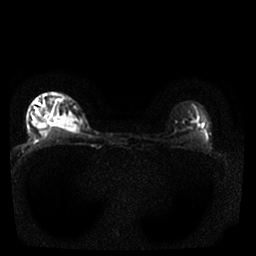
Breast MRI, one axial slice; slice 24 of 25 in the series (ordered by position); diffusion-weighted series; image 2 of 4 stored at this slice position (different b-values; order by instance number); 1.5 T; 4 mm slice thickness; 256 × 256 image matrix, field of view 310 × 310 mm. Female patient.
Outlined on this slice (outlined manually by an expert reader):
- tumour on diffusion-weighted imaging: bounding box [x1, y1, x2, y2] px = [55, 116, 76, 127]